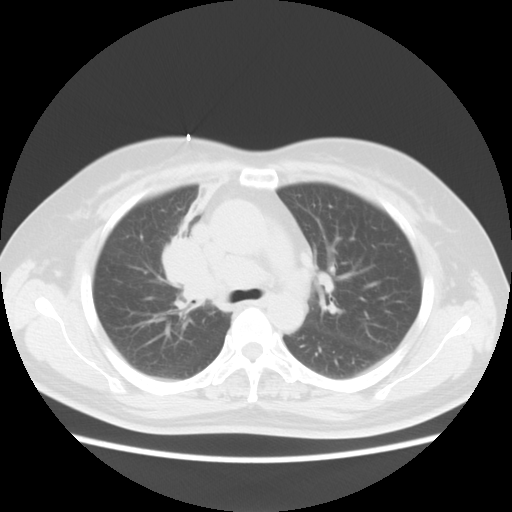
Chest CT, one axial slice. Position 8 of 18 along the scan axis. Reconstruction kernel STANDARD. 120 kVp. Lung window (W 1500 / L -600 HU). 512 × 512 image matrix, field of view 350 × 350 mm. Patient: female, 54 years. Case-level facts recorded for this patient, not image findings: clinical TNM (as recorded): T2 N3 M0.
Structures marked on this image (bounding box drawn by a radiologist):
- lung tumour (recorded histology: small cell carcinoma): box from (x=158, y=240) to (x=219, y=315) px